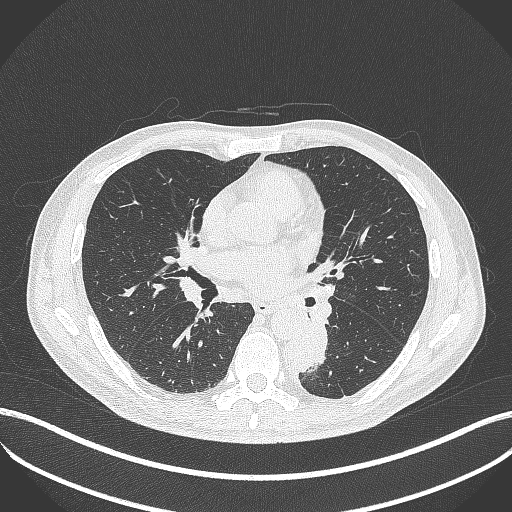
Chest CT, one axial slice; slice 211 of 451 in the series (ordered by position); 120 kVp; lung window (W 1500 / L -600 HU); 512 × 512 image matrix, field of view 400 × 400 mm. Male patient, age 72 years. Case-level facts recorded for this patient, not image findings: clinical TNM (as recorded): T2b N0 M1.
Structures marked on this image (rectangle marked by the reading radiologist):
- lung tumour (recorded histology: adenocarcinoma): bounding box <281,318,339,375> (left, top, right, bottom; pixels)